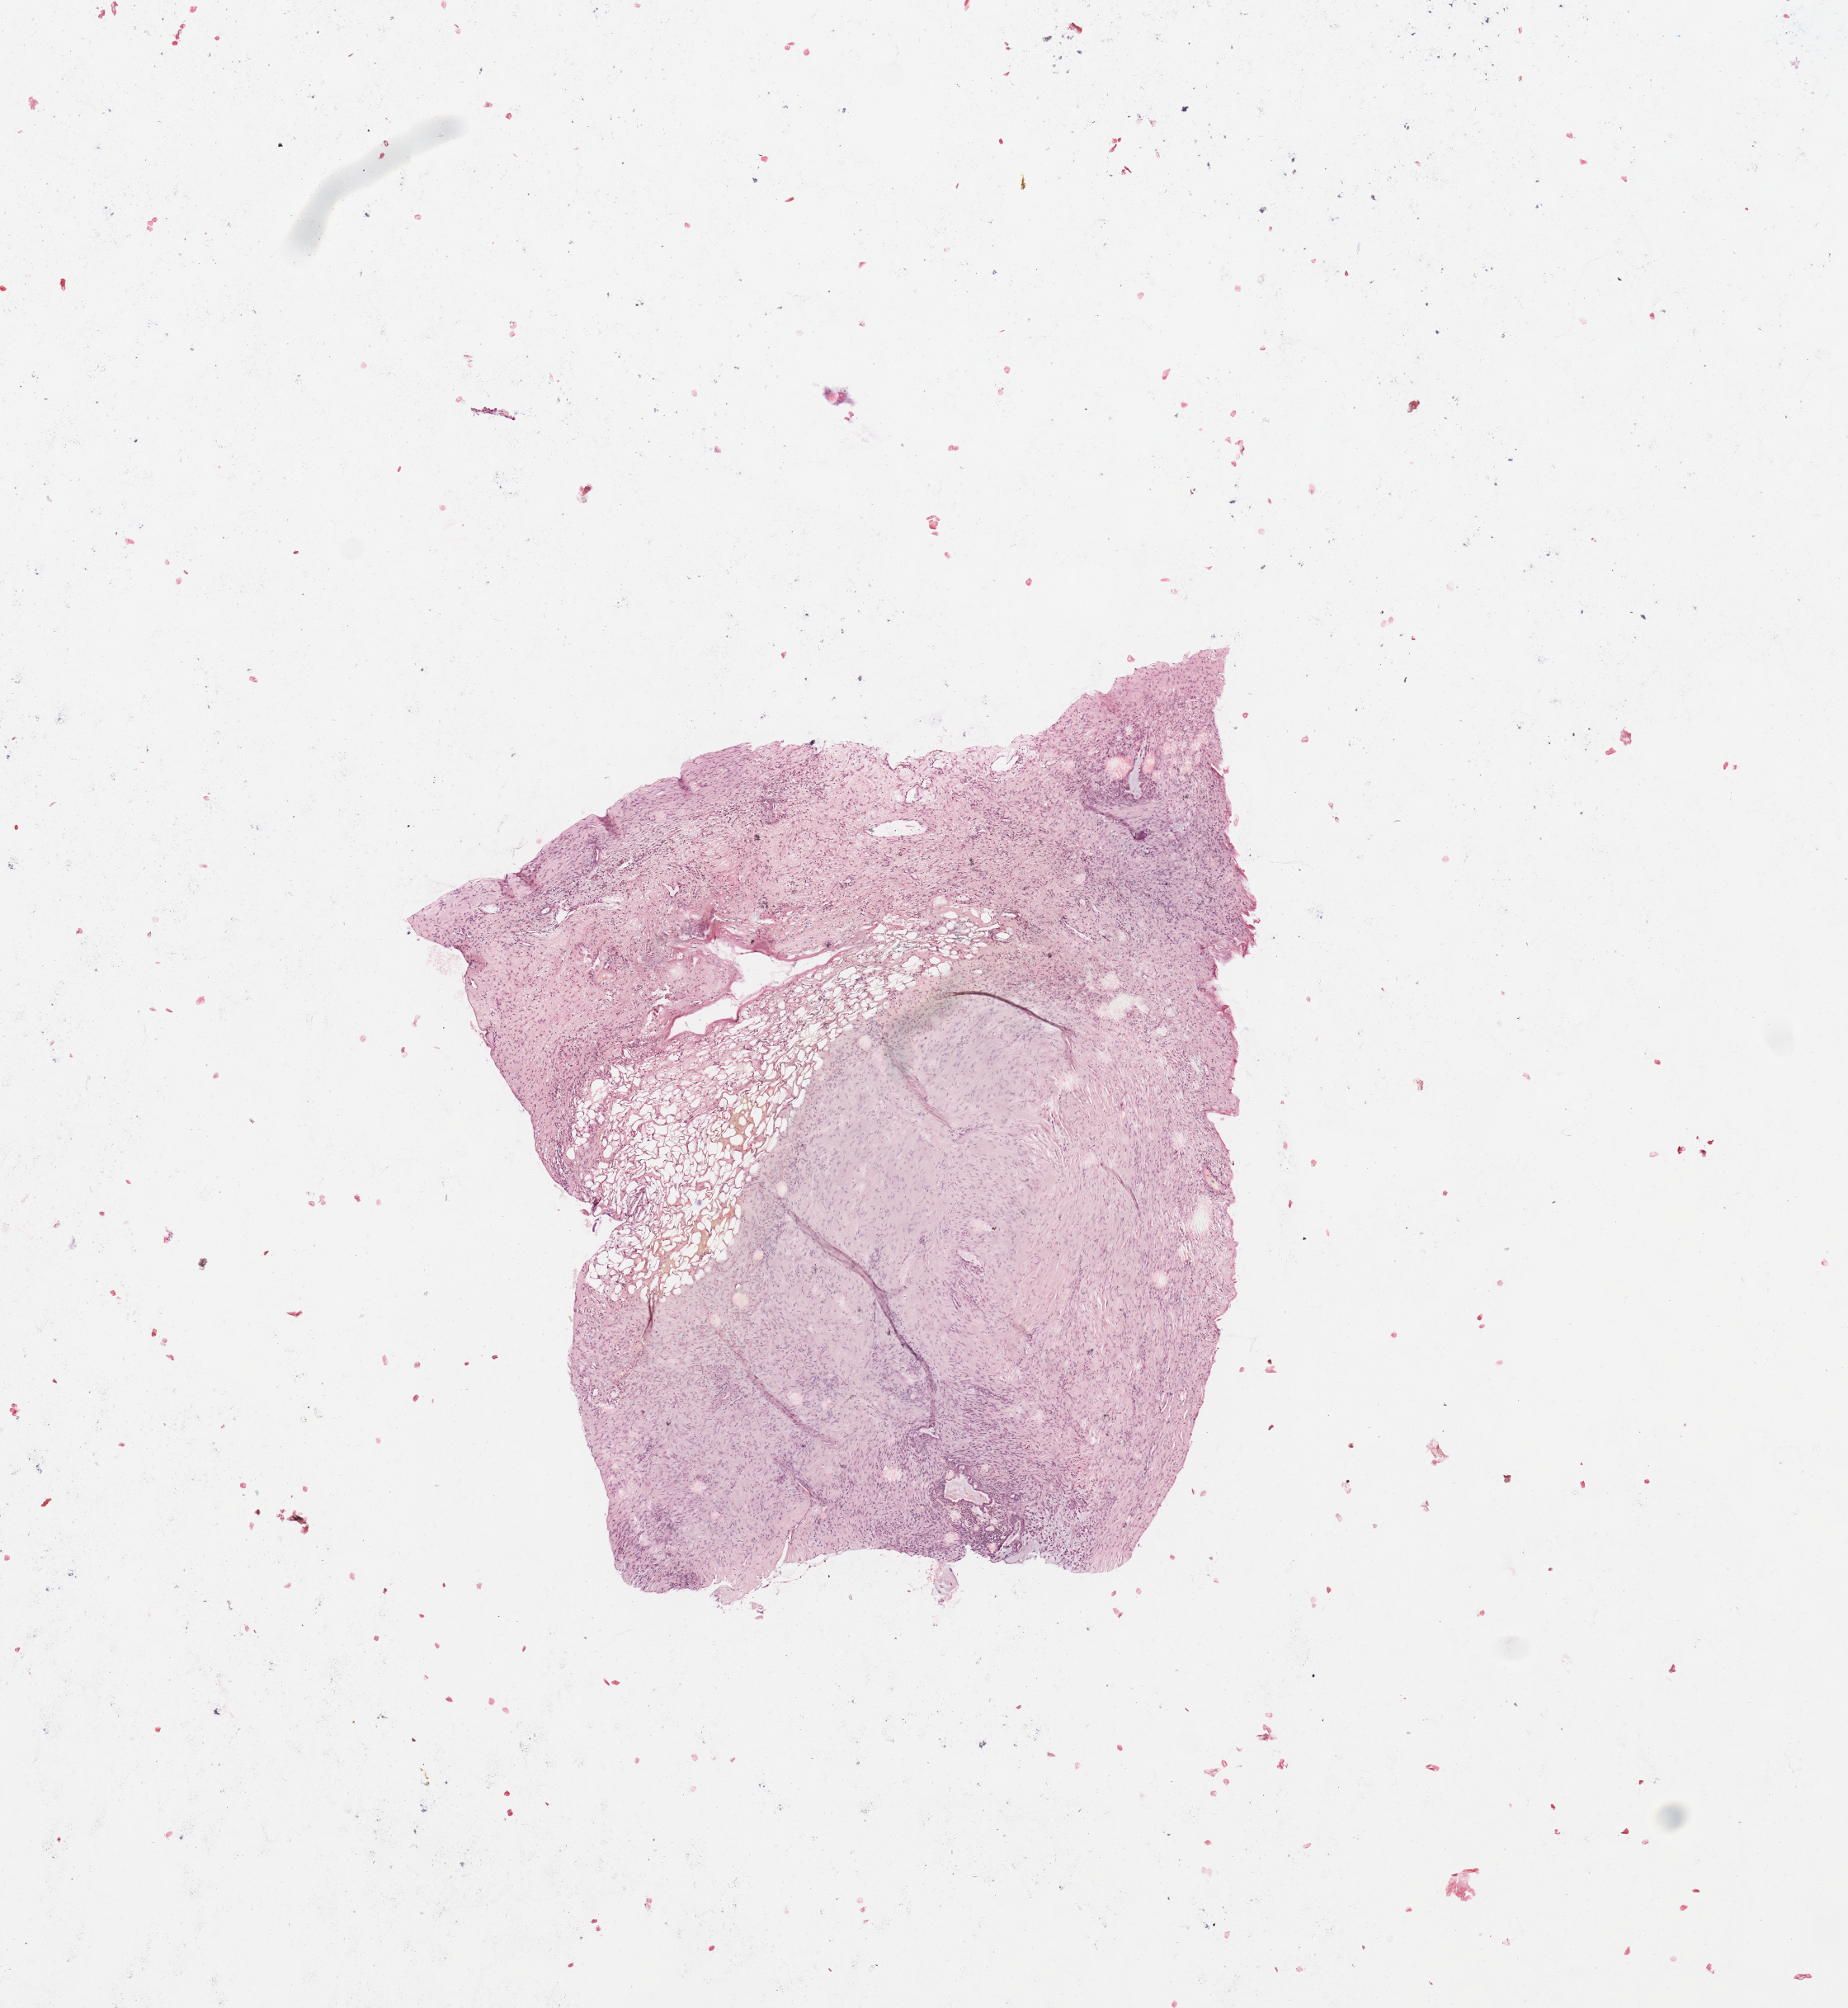
Whole-slide histology image, H&E — shown as a low-resolution overview of the whole scanned area (about 8.9 x 9.6 mm, slide scanned at 20x), pancreas, tumour tissue. Patient: female, age 70 years.
Patient diagnosis (cohort enrolment): ductal adenocarcinoma (pancreas).